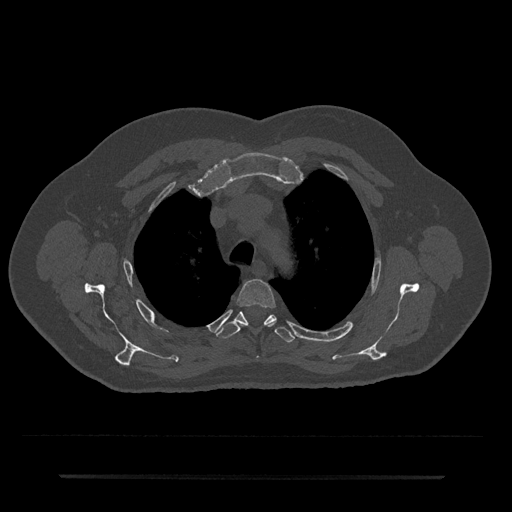
CT including the spine, one axial slice. Slice 548 of 797 in the series (ordered by position). Reconstruction kernel Br40s/3. 120 kVp. Bone window (W 1800 / L 400 HU). 0.5 mm slice thickness. 512 × 512 image matrix, field of view 437 × 437 mm. Patient: male, 69 years. Case-level facts recorded for this patient, not image findings: primary cancer: prostate.
Annotated regions visible in this slice (semi-automatic segmentation, software-assisted and operator-edited):
- T3 vertebra: box from (x=237, y=279) to (x=275, y=358) px
- T4 vertebra: (x=216, y=311)–(x=295, y=343)